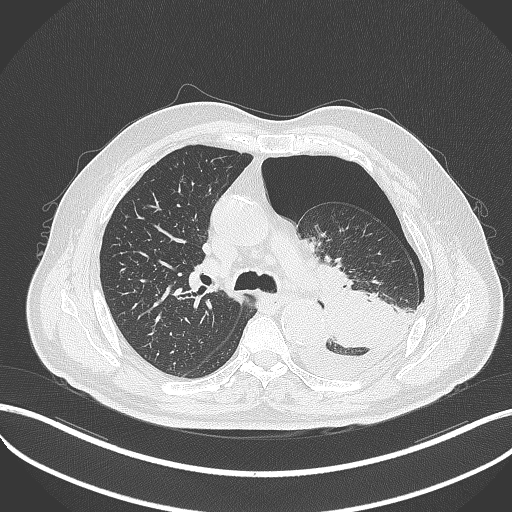
Chest CT, one axial slice; slice 336 of 464 in the series (ordered by position); reconstruction kernel B70f; lung window (W 1500 / L -600 HU); 1 mm slice thickness; 512 × 512 image matrix, field of view 400 × 400 mm. Patient: male, 76 years. Case-level facts recorded for this patient, not image findings: clinical TNM (as recorded): T3 N0 M1b.
Annotated regions visible in this slice (rectangle marked by the reading radiologist):
- lung tumour (recorded histology: adenocarcinoma): bounding box <319,278,394,352> (left, top, right, bottom; pixels)